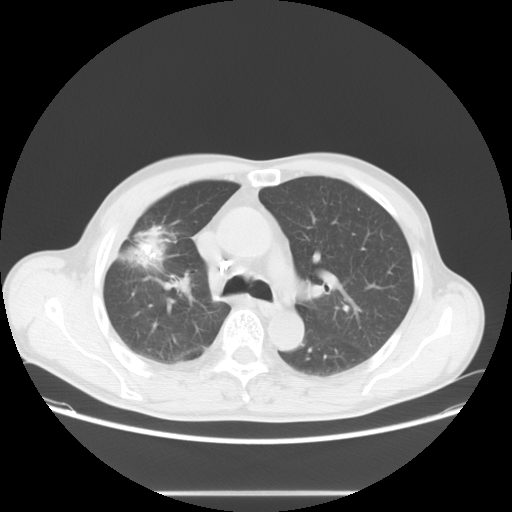
Chest CT, one axial slice. Position 45 of 69 along the scan axis. Reconstruction kernel STANDARD. Lung window (W 1500 / L -600 HU). 512 × 512 image matrix. Male patient, age 67 years. Case-level facts recorded for this patient, not image findings: clinical TNM (as recorded): T2 N0 M0.
Outlined on this slice (rectangle marked by the reading radiologist):
- lung tumour (recorded histology: adenocarcinoma): box from (x=134, y=228) to (x=172, y=268) px